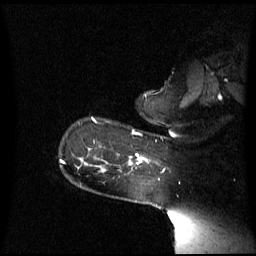
Breast MRI (dynamic contrast-enhanced), one sagittal slice; slice 51 of 60 in the series (ordered by position); dynamic contrast-enhanced series, image 2 of 3 at this slice position (ordered by acquisition); 1.5 T; TE 4.2 ms, TR 8.4 ms; 256 × 256 image matrix, field of view 270 × 270 mm. Patient: female, 39 years. Case-level facts recorded for this patient, not image findings: setting: breast cancer imaged before/during neoadjuvant chemotherapy; receptor status: triple-negative.
Structures marked on this image (semi-automatic segmentation, software-assisted and operator-edited):
- analysis volume of interest (the breast-tissue region the enhancement analysis was run in; not a lesion): box from (x=120, y=154) to (x=147, y=171) px
- tumour enhancement mask (voxels above the 70 % enhancement threshold inside the analysis volume of interest): (x=139, y=157)–(x=146, y=161)